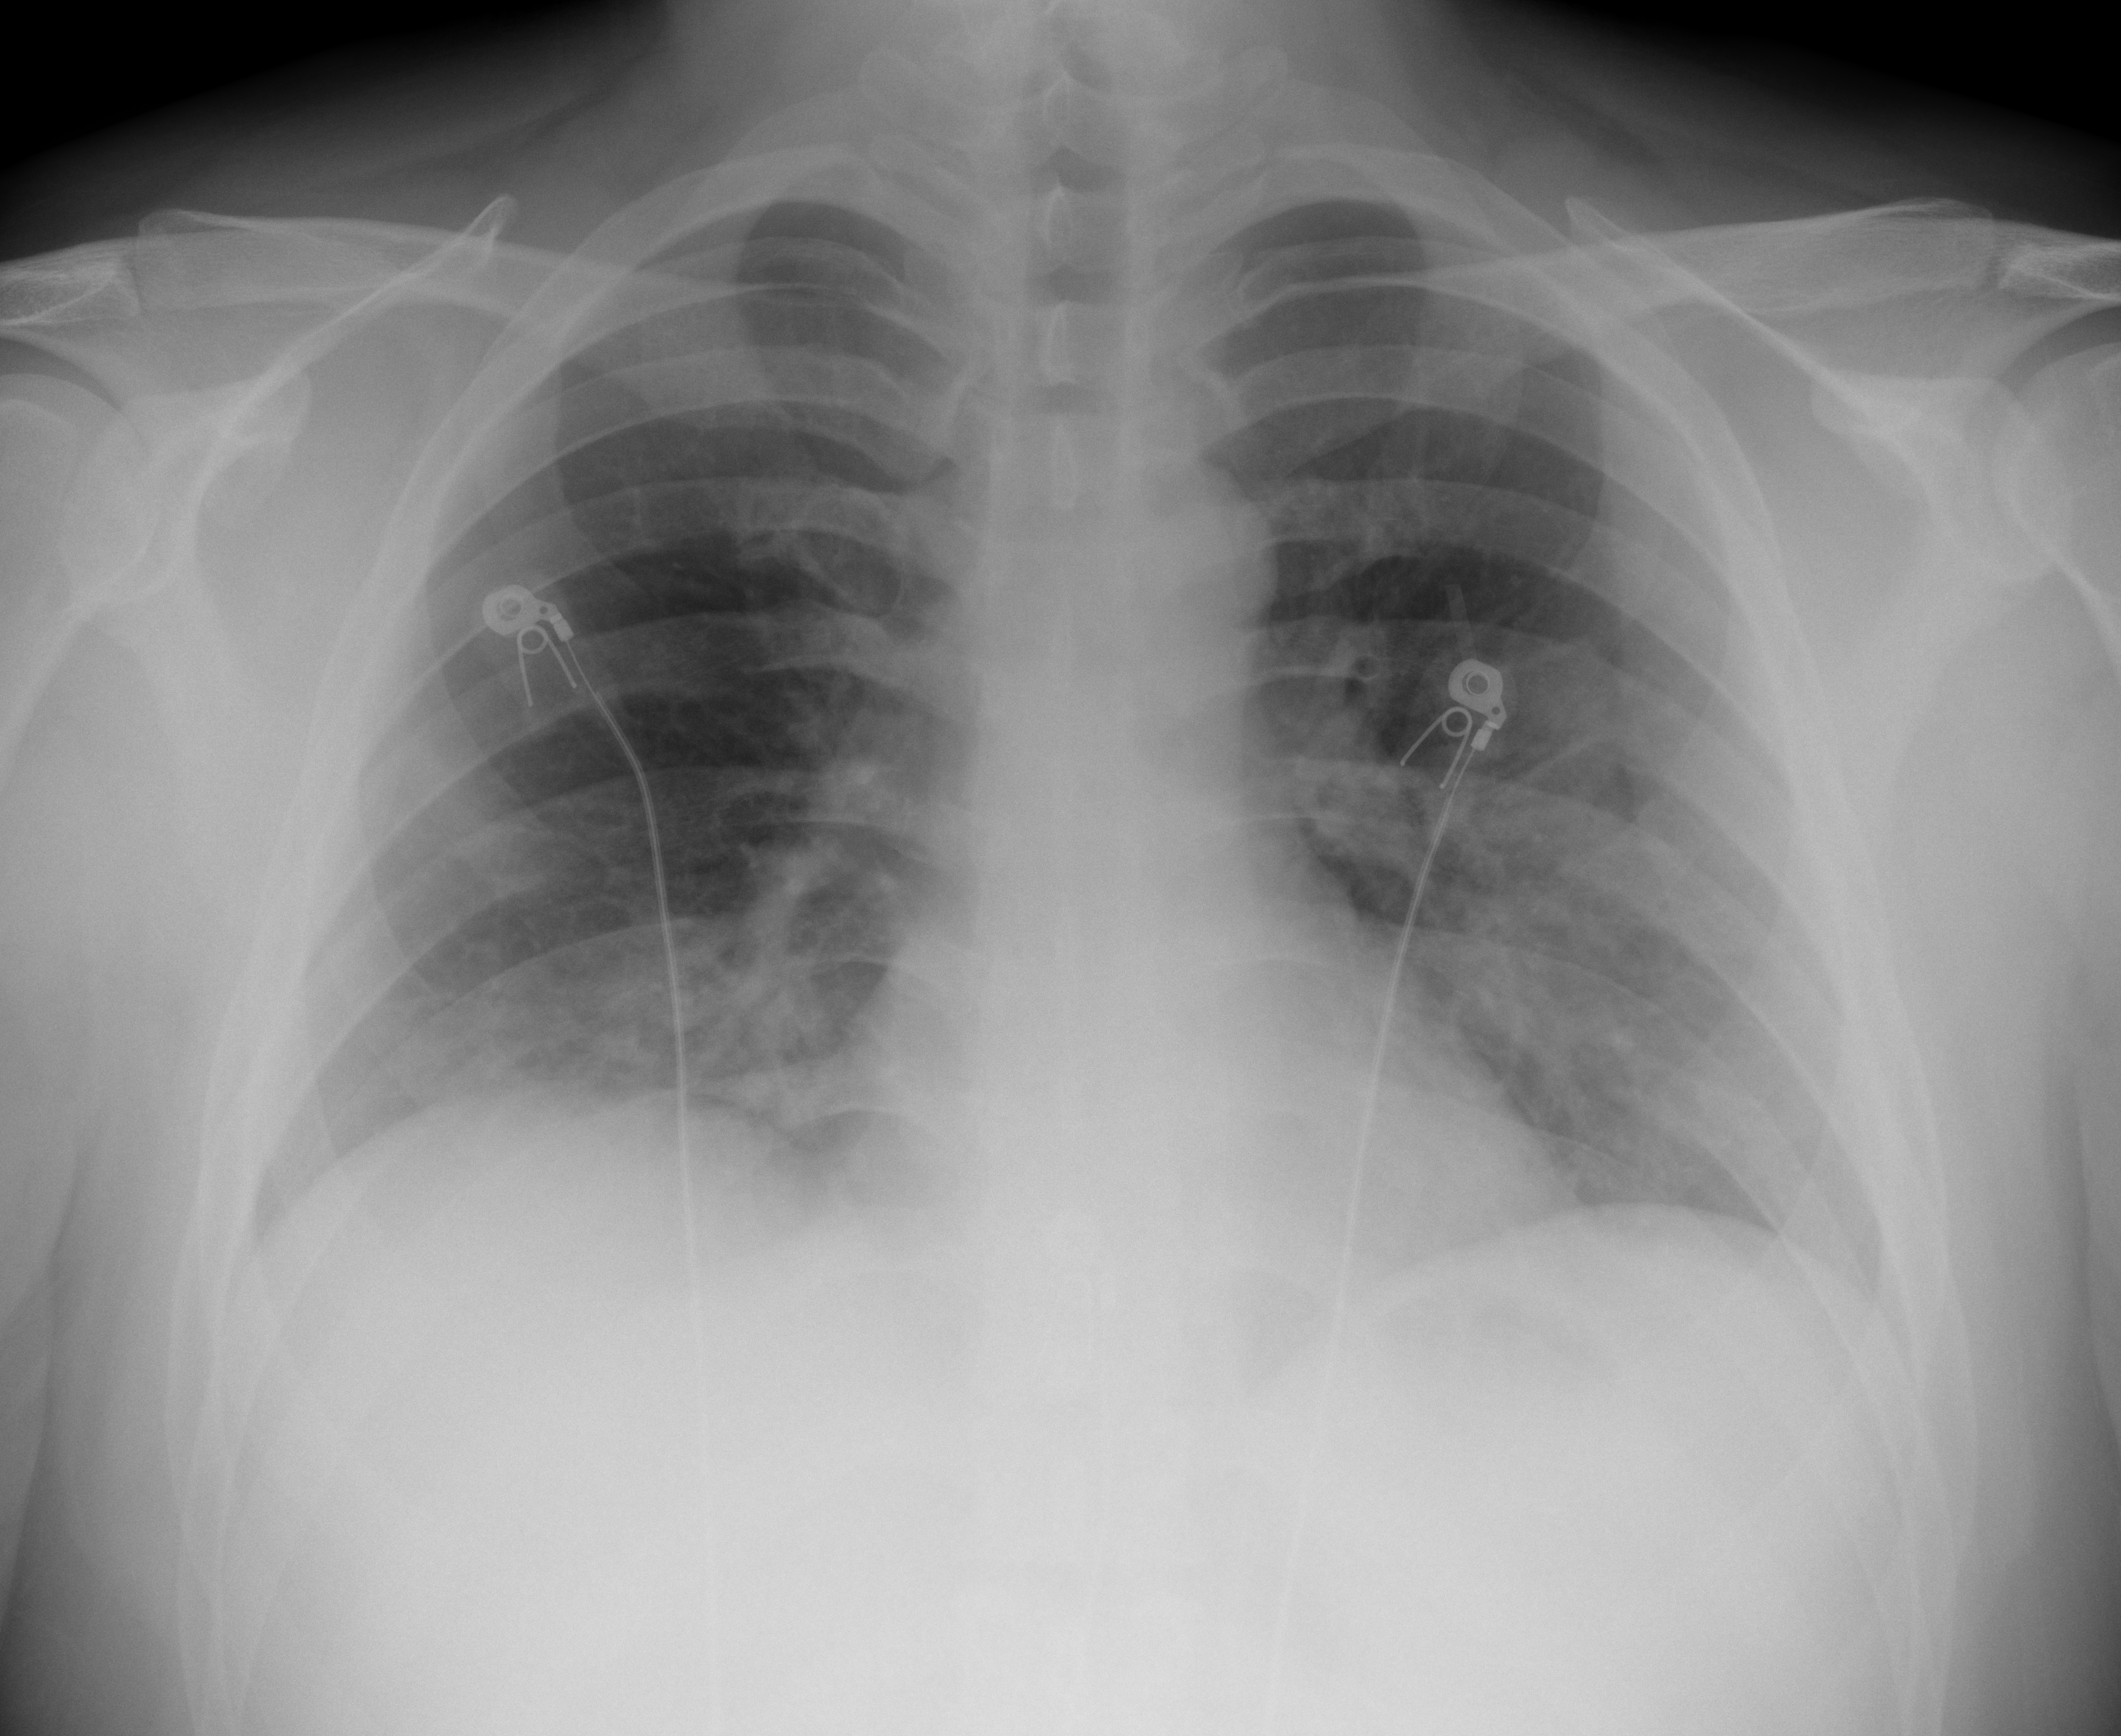
Chest X-ray (portable), AP projection. Male patient, age 38 years; imaged 0 days after the COVID-19 diagnosis.
Radiologist key findings (as recorded): patchy areas of ill-defined consolidation in both lower lobes. The upper lungs are still clear.